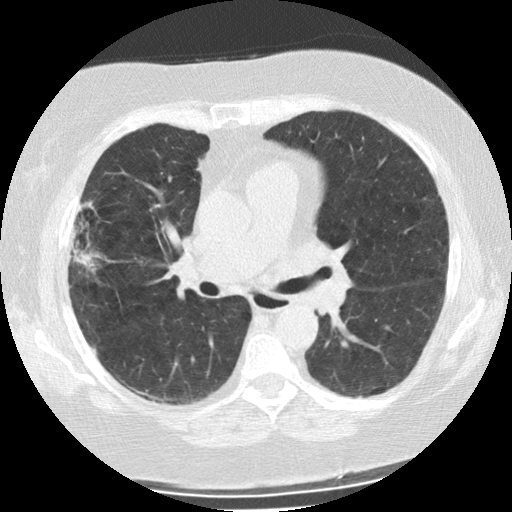
Low-dose screening chest CT, one axial slice; position 133 of 225 along the scan axis; reconstruction kernel STANDARD; 120 kVp; lung window (W 1500 / L -600 HU); 512 × 512 image matrix, field of view 320 × 320 mm.
Outlined on this slice (expert manual segmentation):
- lesion 1 (tumor, upper lobe of right lung): bounding box <73,225,101,273> (left, top, right, bottom; pixels)